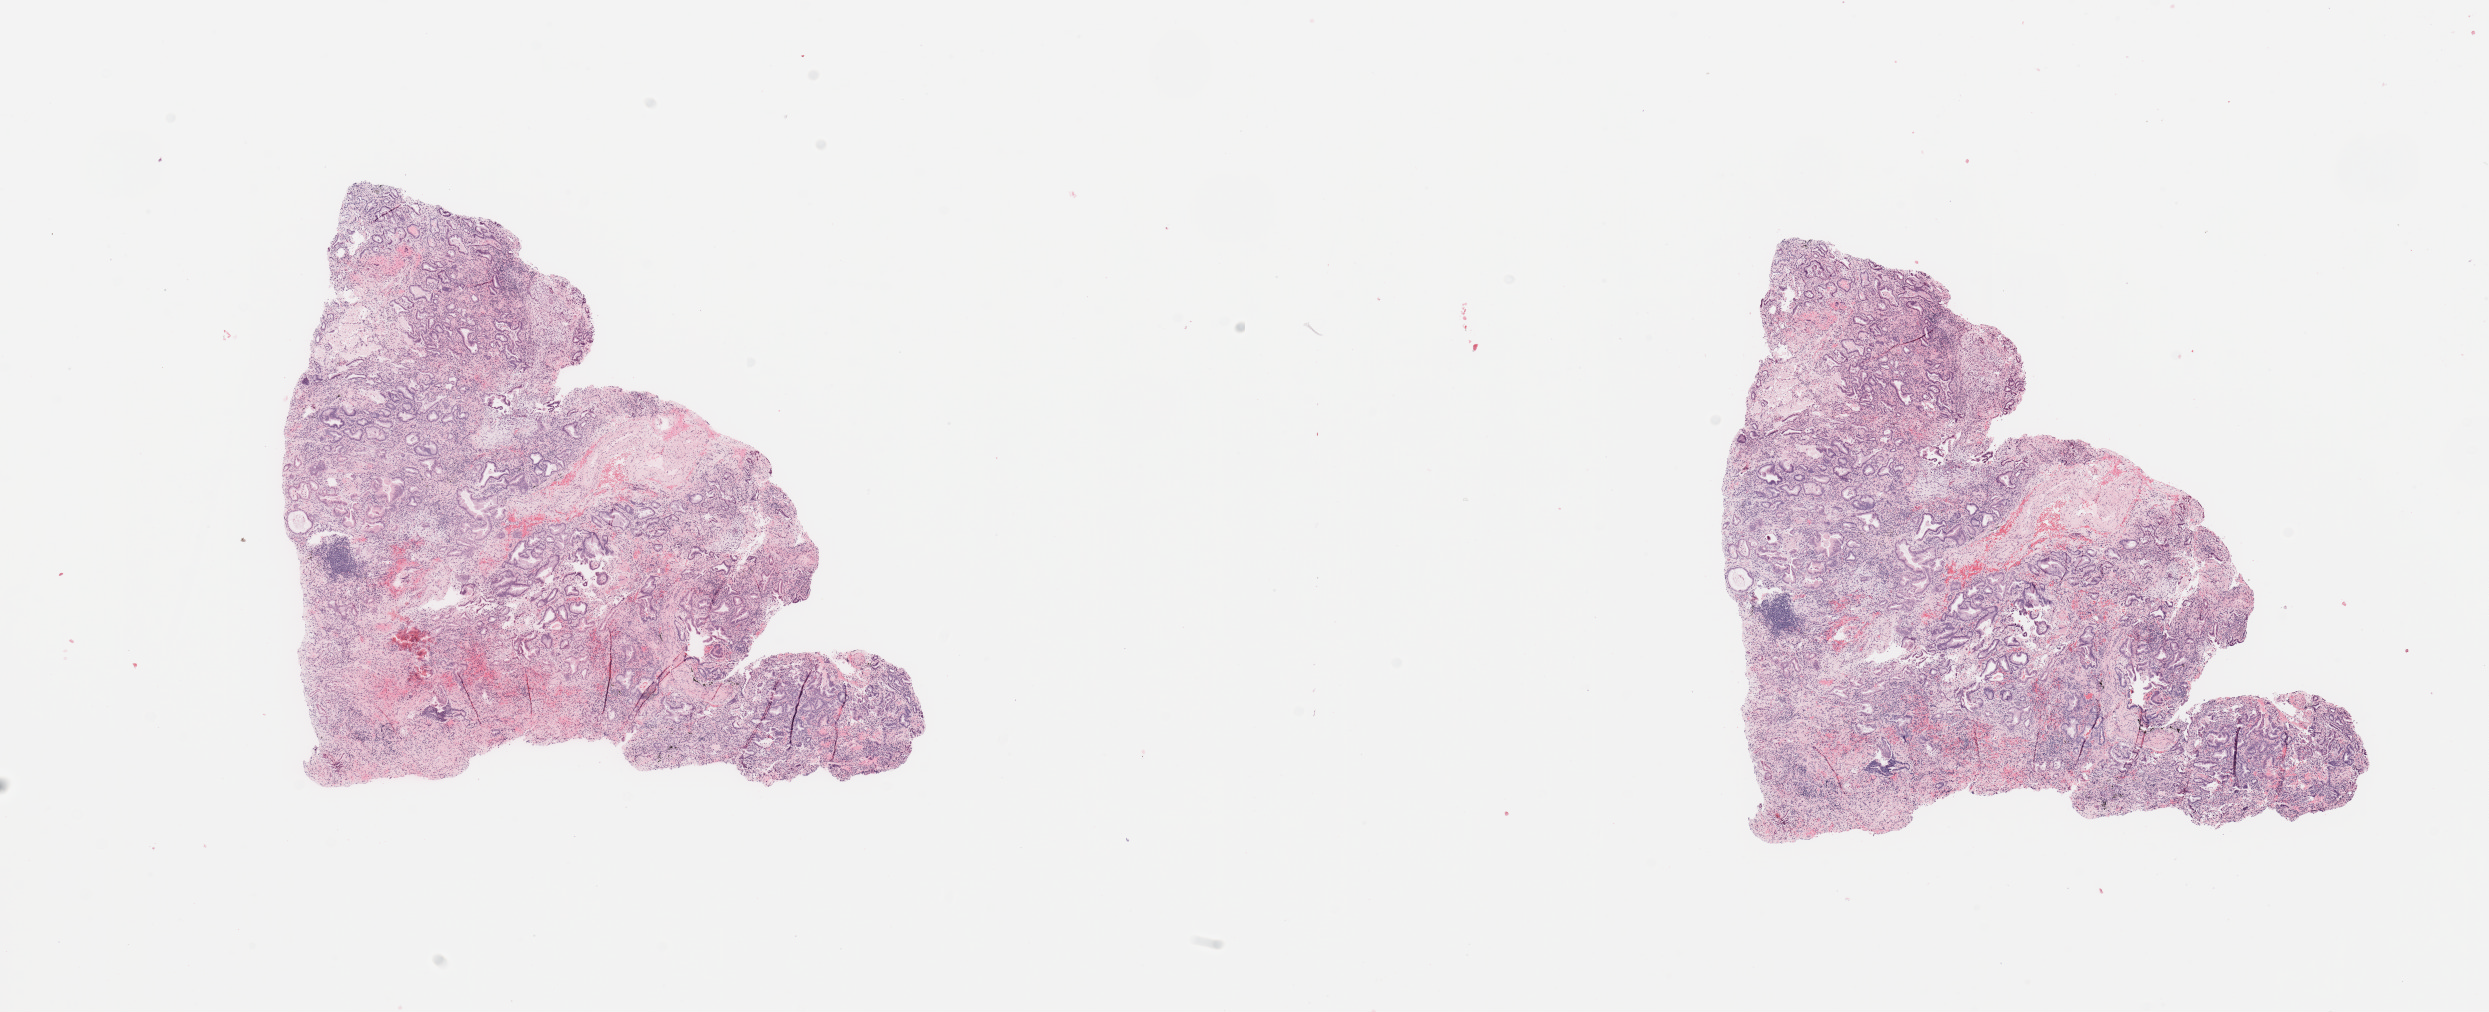
H&E whole-slide image — shown as a low-resolution overview of the whole scanned area (about 19.7 x 8.0 mm, from a 20x scan); tumour tissue sample, sampled site: lung. Male, 46 y/o. Histologic grade: G2 (moderately differentiated). Composition of this section per pathologist review: tumour nuclei 70%, necrosis 5%.
- diagnosis: Adenocarcinoma, NOS